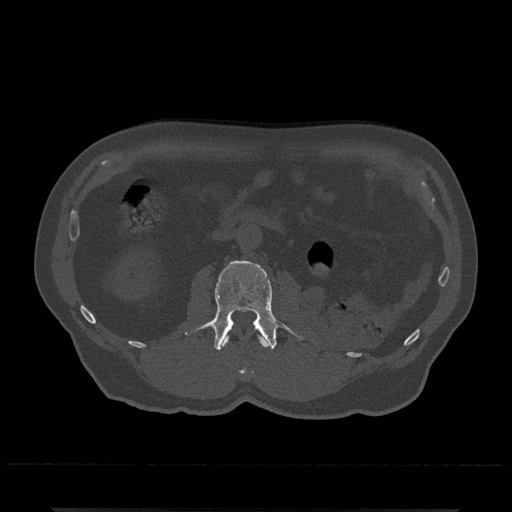
CT including the spine, one axial slice; position 304 of 797 along the scan axis; bone window (W 1800 / L 400 HU); 0.5 mm slice thickness; 512 × 512 image matrix. Patient: male, 67 years. Case-level facts recorded for this patient, not image findings: primary cancer: prostate.
Structures marked on this image (semi-automatically segmented with operator editing):
- L1 vertebra: bounding box [x1, y1, x2, y2] px = [222, 335, 269, 375]
- L2 vertebra: [184, 260, 304, 350]